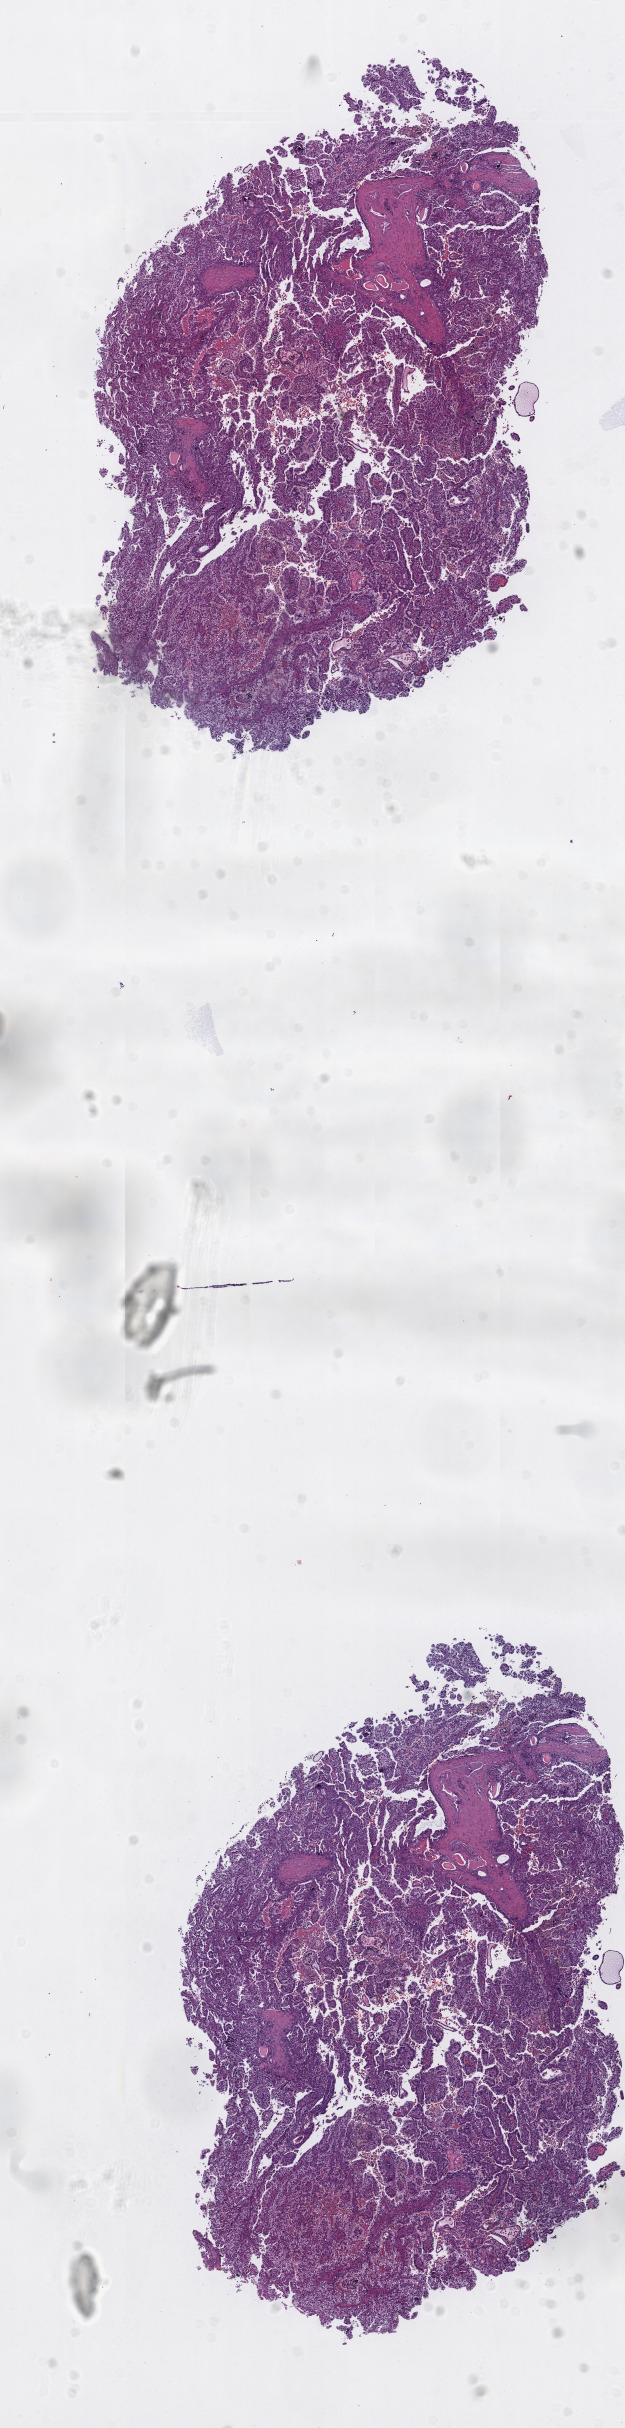
Digitized Hematoxylin and eosin (H&E) stained tissue section (whole slide), a low-resolution overview of the entire scanned area, about 5.0 x 19.5 mm (acquisition: 20x scan); frozen section from the top of the tissue portion; primary tumour sample from the kidney. Male patient; age at initial diagnosis 52 years. Pathologist review of this section (percent, as recorded): tumour cells 88%, tumour nuclei 85%, normal cells 0%, stromal cells 12%, necrosis 0%.
Laterality: left. AJCC pathologic stage: III. Histologic diagnosis: Papillary adenocarcinoma, NOS.